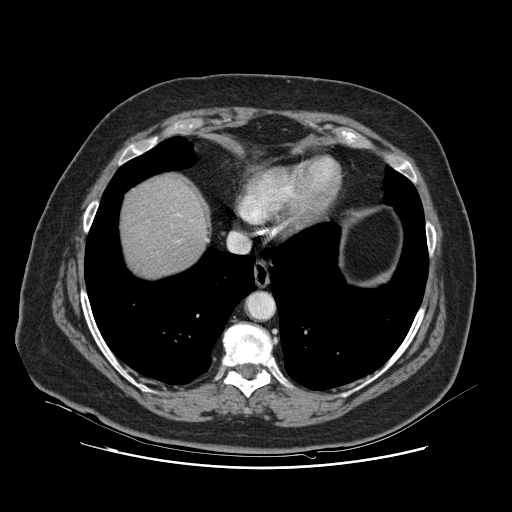
Contrast-enhanced abdominal CT, one axial slice; slice 113 of 132 in the series (ordered by position); 120 kVp; intravenous contrast given; soft-tissue window (W 400 / L 40 HU); 2.5 mm slice thickness; 512 × 512 image matrix. Female patient, age 73 years. From the clinical record (not read from this slice): diagnosis: colorectal cancer liver metastases, imaged before liver resection; multiple liver metastases: no; largest metastasis: 7 cm; chemotherapy before resection: yes.
Annotated regions visible in this slice (expert manual segmentation):
- liver: bounding box [x1, y1, x2, y2] px = [121, 177, 207, 279]
- planned liver remnant (the part of the liver to remain after resection): [121, 176, 206, 278]